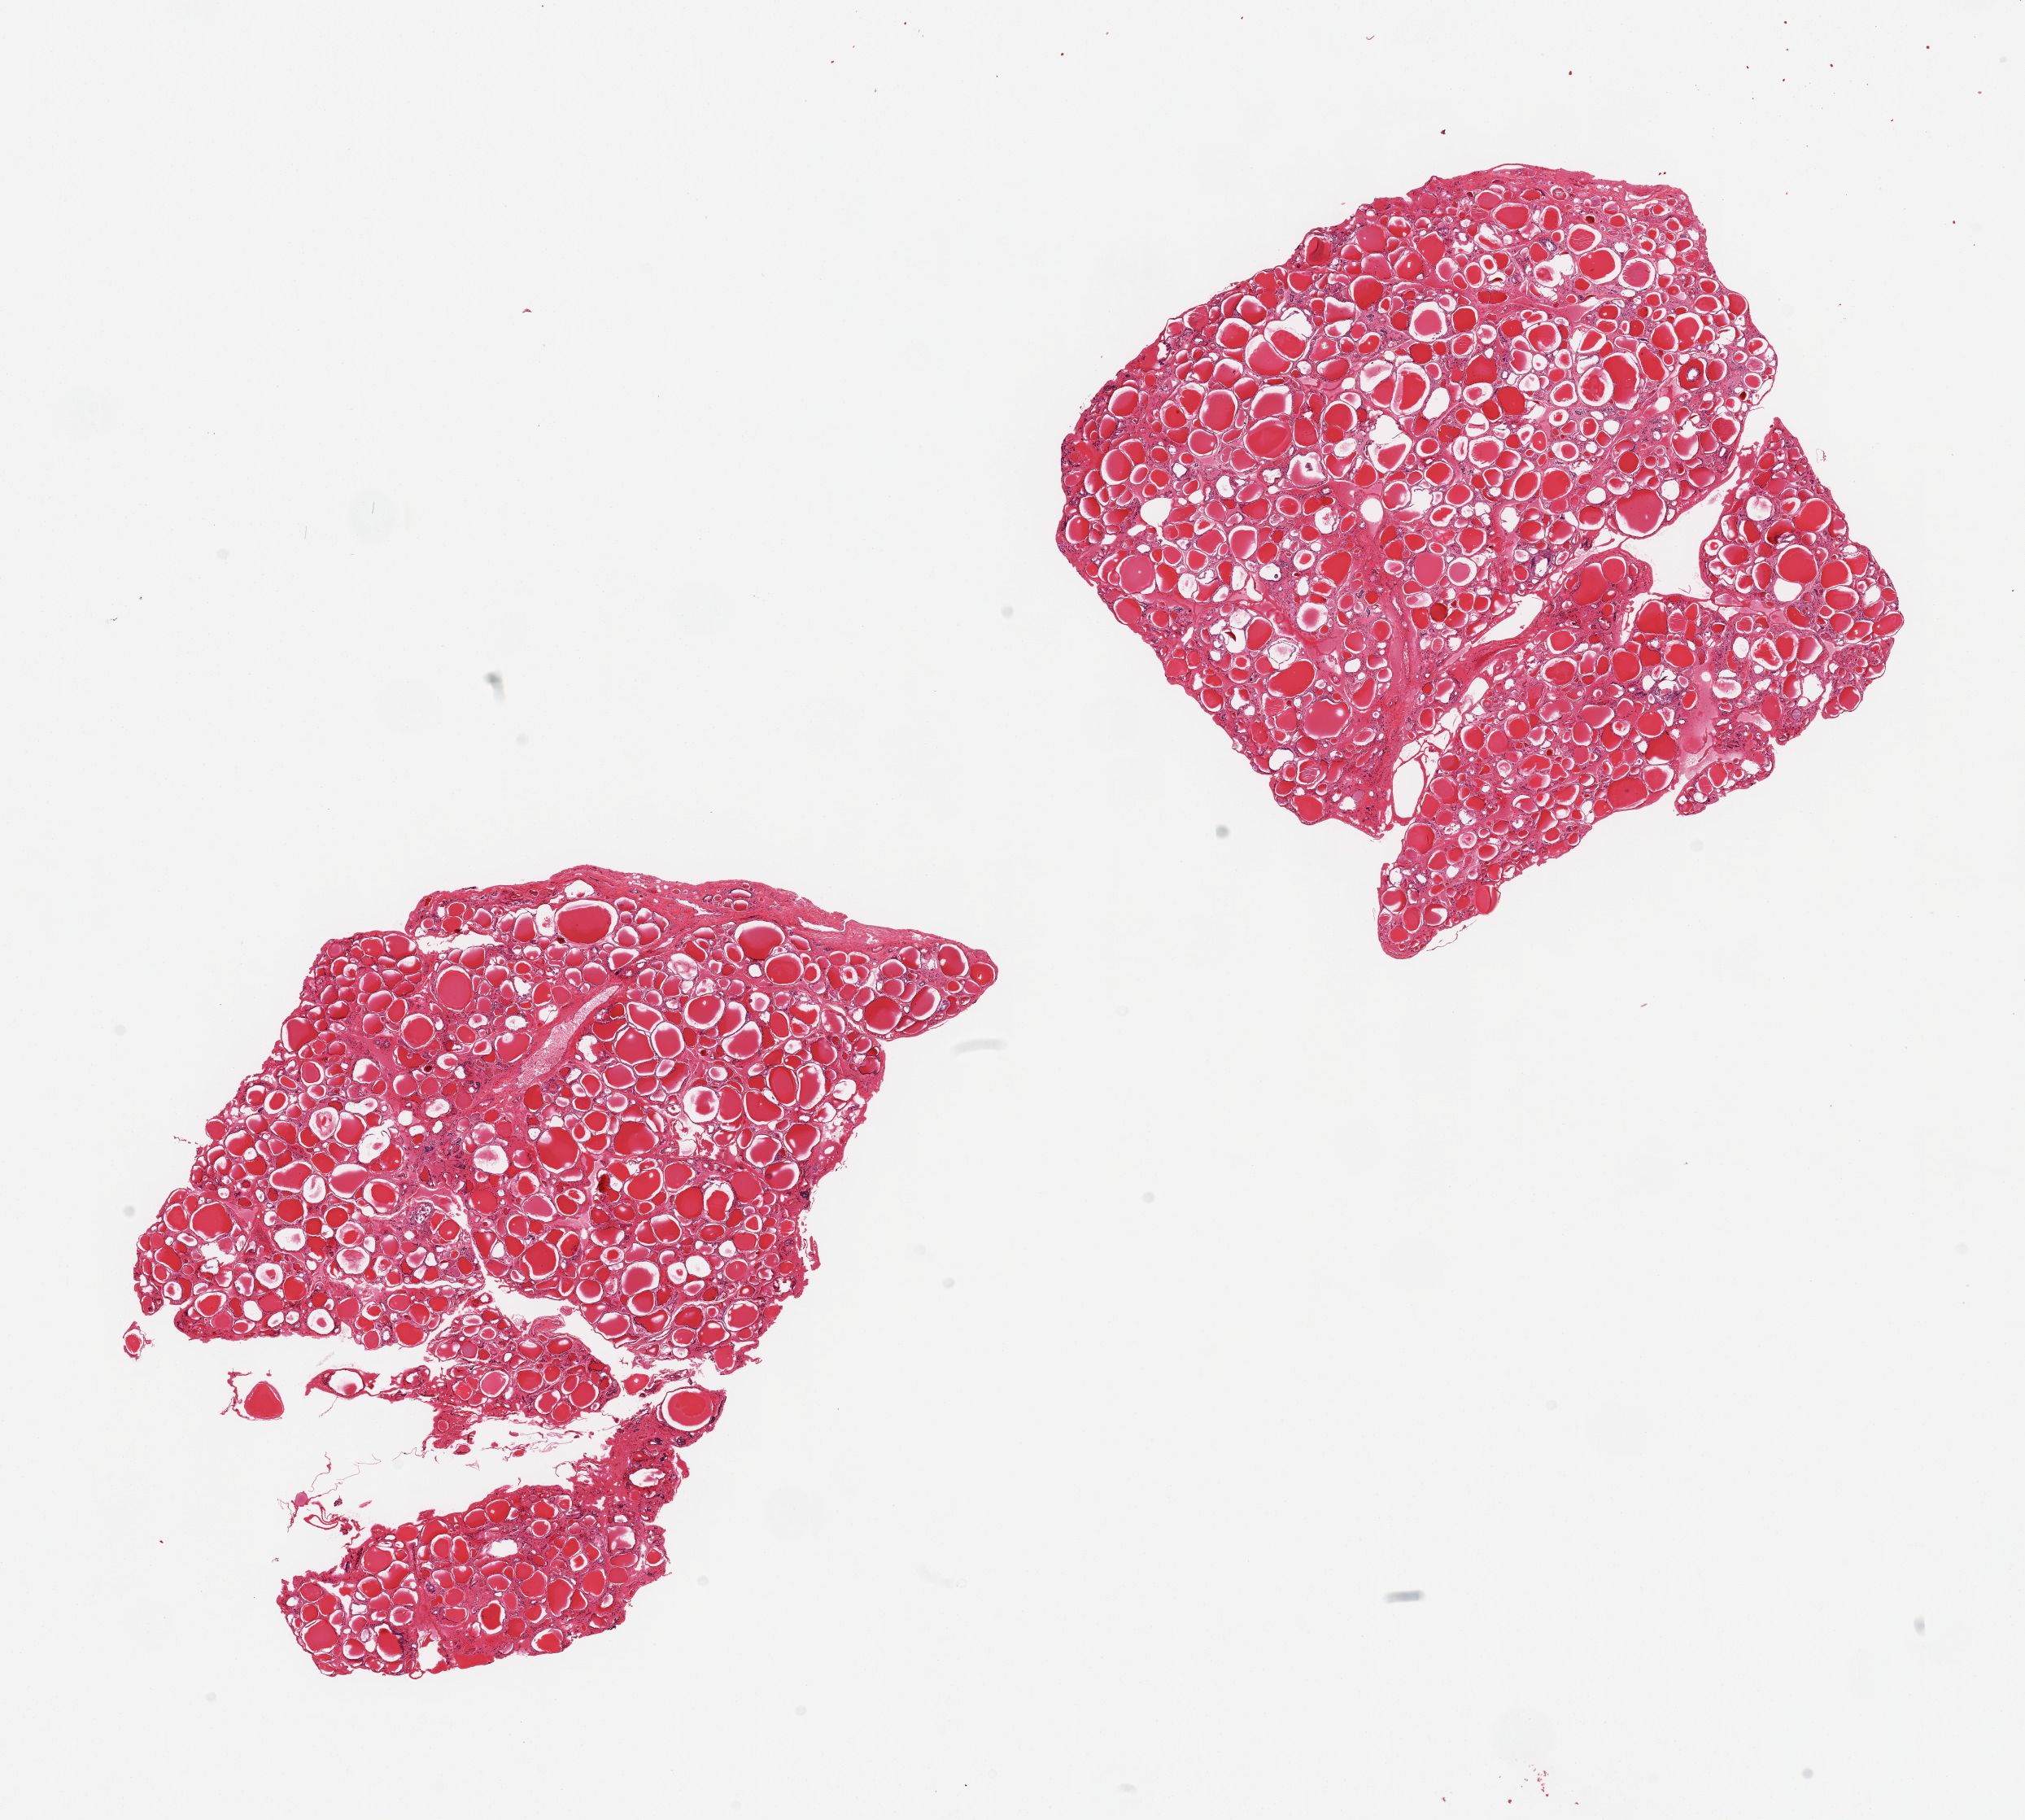
Digitized haematoxylin and eosin-stained section, shown as a low-resolution overview of the whole scanned area (about 19.7 x 17.7 mm); PAXgene-fixed paraffin-embedded (PFPE) section; target tissue: thyroid; tissue donor sample. Donor sex: male.
* review note (as recorded): 2 pieces, no abnormalities